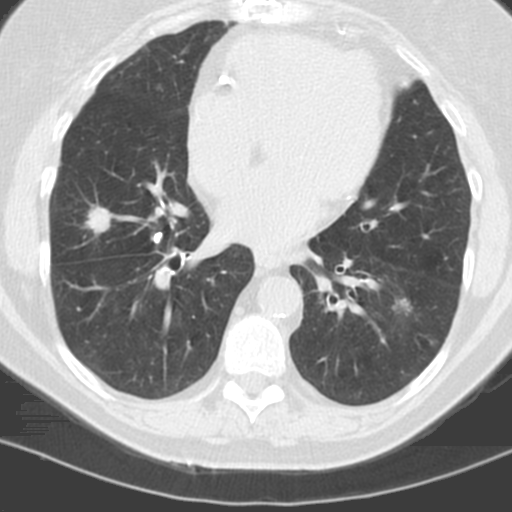
Chest CT (low-dose screening protocol), one axial image, baseline annual screen, lung window (W 1500 / L -600 HU), 3.2 mm slice thickness, standard (soft-tissue) reconstruction kernel (C). Female, age 60 years at enrolment.
• Expert reader's lesion annotation, bounding box (x1, y1, x2, y2) in pixels: (377, 286, 423, 327).
• The screening reader recorded 3 non-calcified nodules or masses ≥4 mm on this exam (left lower lobe, left lower lobe, right middle lobe); which of them this box marks is not recorded.
• Official screen result: positive, change unspecified: nodule(s) >= 4 mm or enlarging nodule(s), mass(es), or other non-specific abnormalities suspicious for lung cancer.
• Participant outcome: lung cancer diagnosed 96 days after this screen — adenocarcinoma, NOS, left lower lobe, stage IV (AJCC 6th edition), 22 mm at pathology.